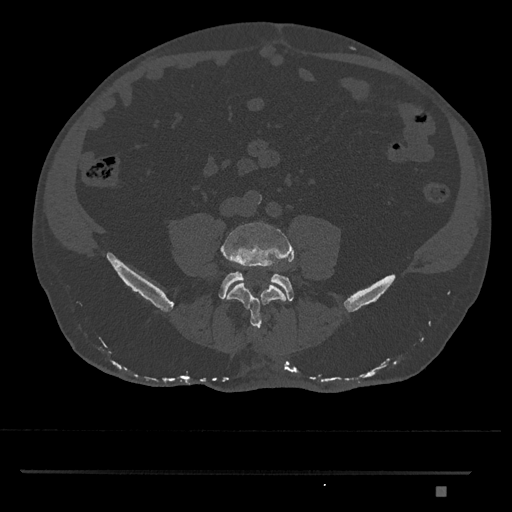
CT including the spine, one axial slice; position 589 of 1134 along the scan axis; bone window (W 1800 / L 400 HU); 512 × 512 image matrix, field of view 429 × 429 mm. Male patient, age 65 years. From the clinical record (not read from this slice): primary cancer: prostate.
Structures marked on this image (semi-automatically segmented with operator editing):
- L4 vertebra: bounding box (x1, y1, x2, y2) in pixels: (221, 222, 294, 329)
- L5 vertebra: (219, 272, 294, 301)